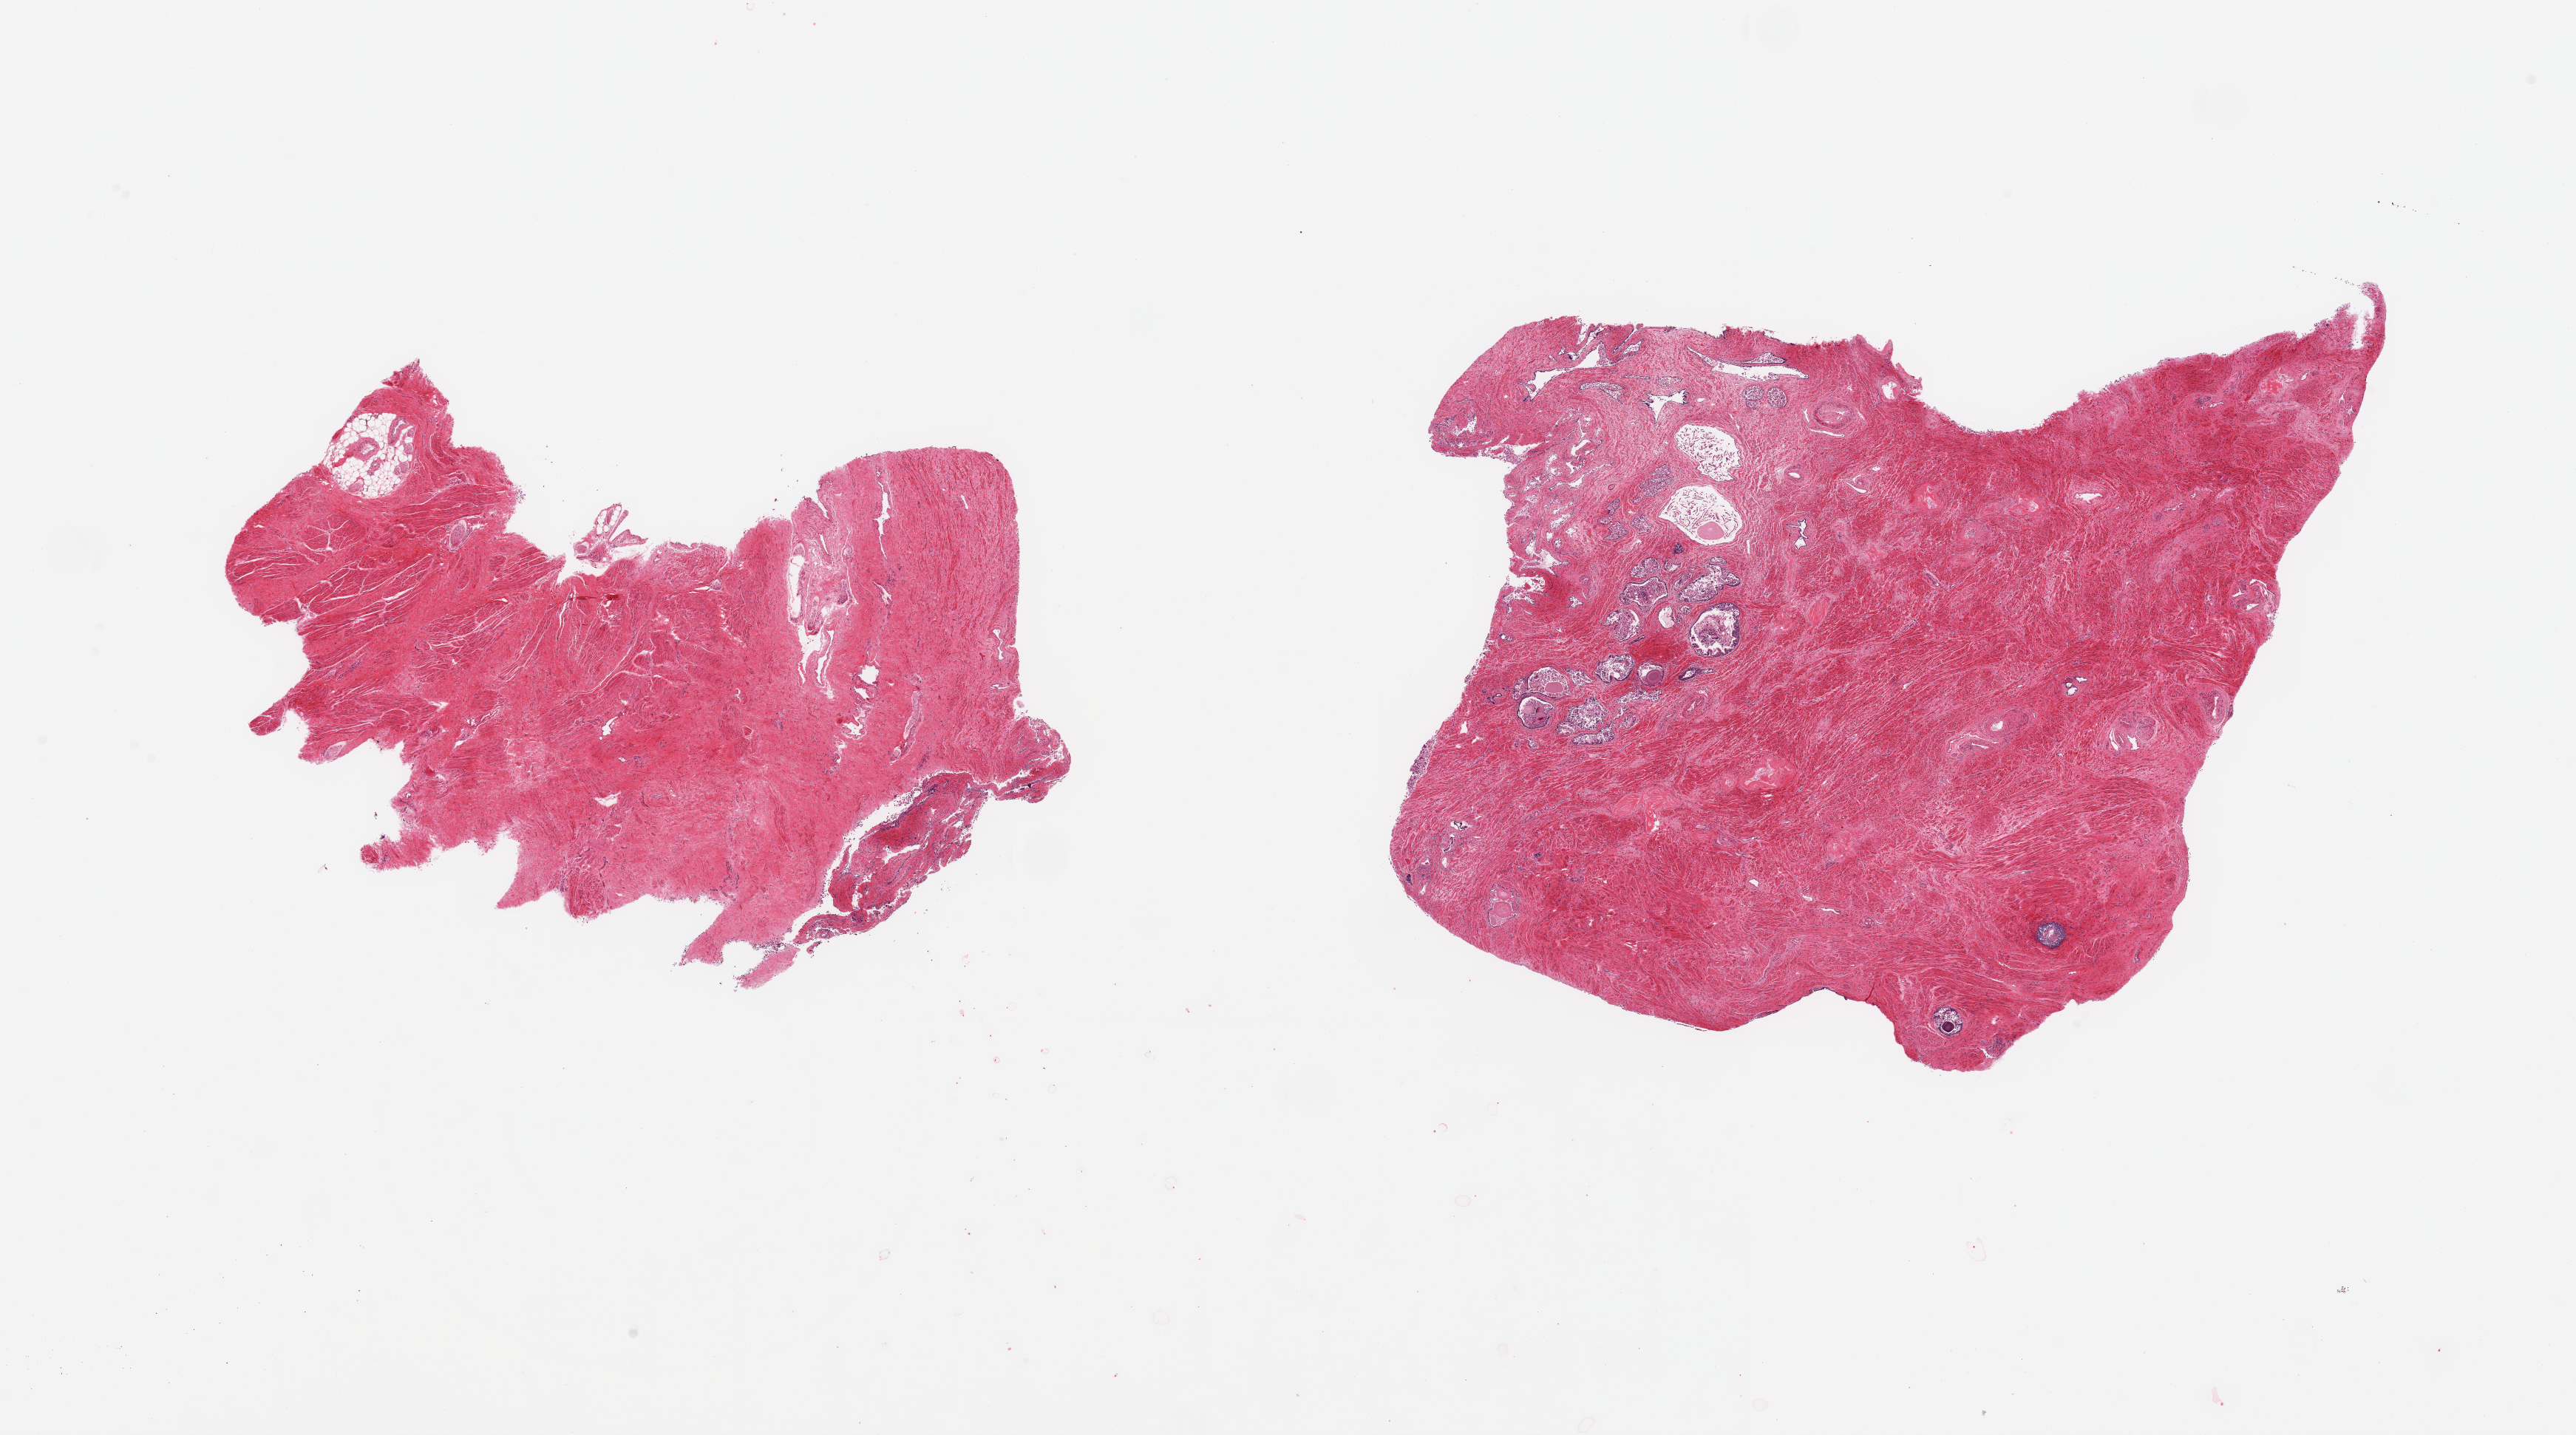
H&E whole-slide image, whole scanned area (about 27.6 x 15.4 mm, acquisition: 20x scan) shown as a low-resolution overview, PAXgene-fixed, paraffin-embedded tissue, sampled site (target tissue): prostate, tissue donor sample. Male donor.
• review note (as recorded): 2 pieces: 1 is all stroma; other contains glands which are largely autolyzed; stroma preserved